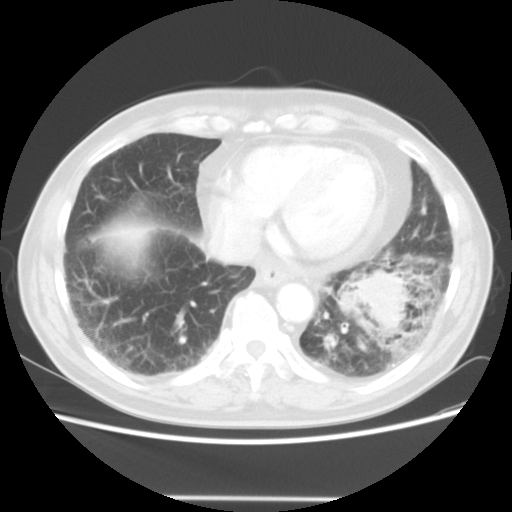
Chest CT, one axial slice. Position 14 of 56 along the scan axis. Reconstruction kernel STANDARD. 140 kVp. Lung window (W 1500 / L -600 HU). 5 mm slice thickness. 512 × 512 image matrix, field of view 360 × 360 mm. Male patient, age 66 years. From the clinical record (not read from this slice): clinical TNM (as recorded): T4 N3 M0.
Annotated regions visible in this slice (rectangle marked by the reading radiologist):
- lung tumour (recorded histology: small cell carcinoma): bounding box <326,262,416,353> (left, top, right, bottom; pixels)